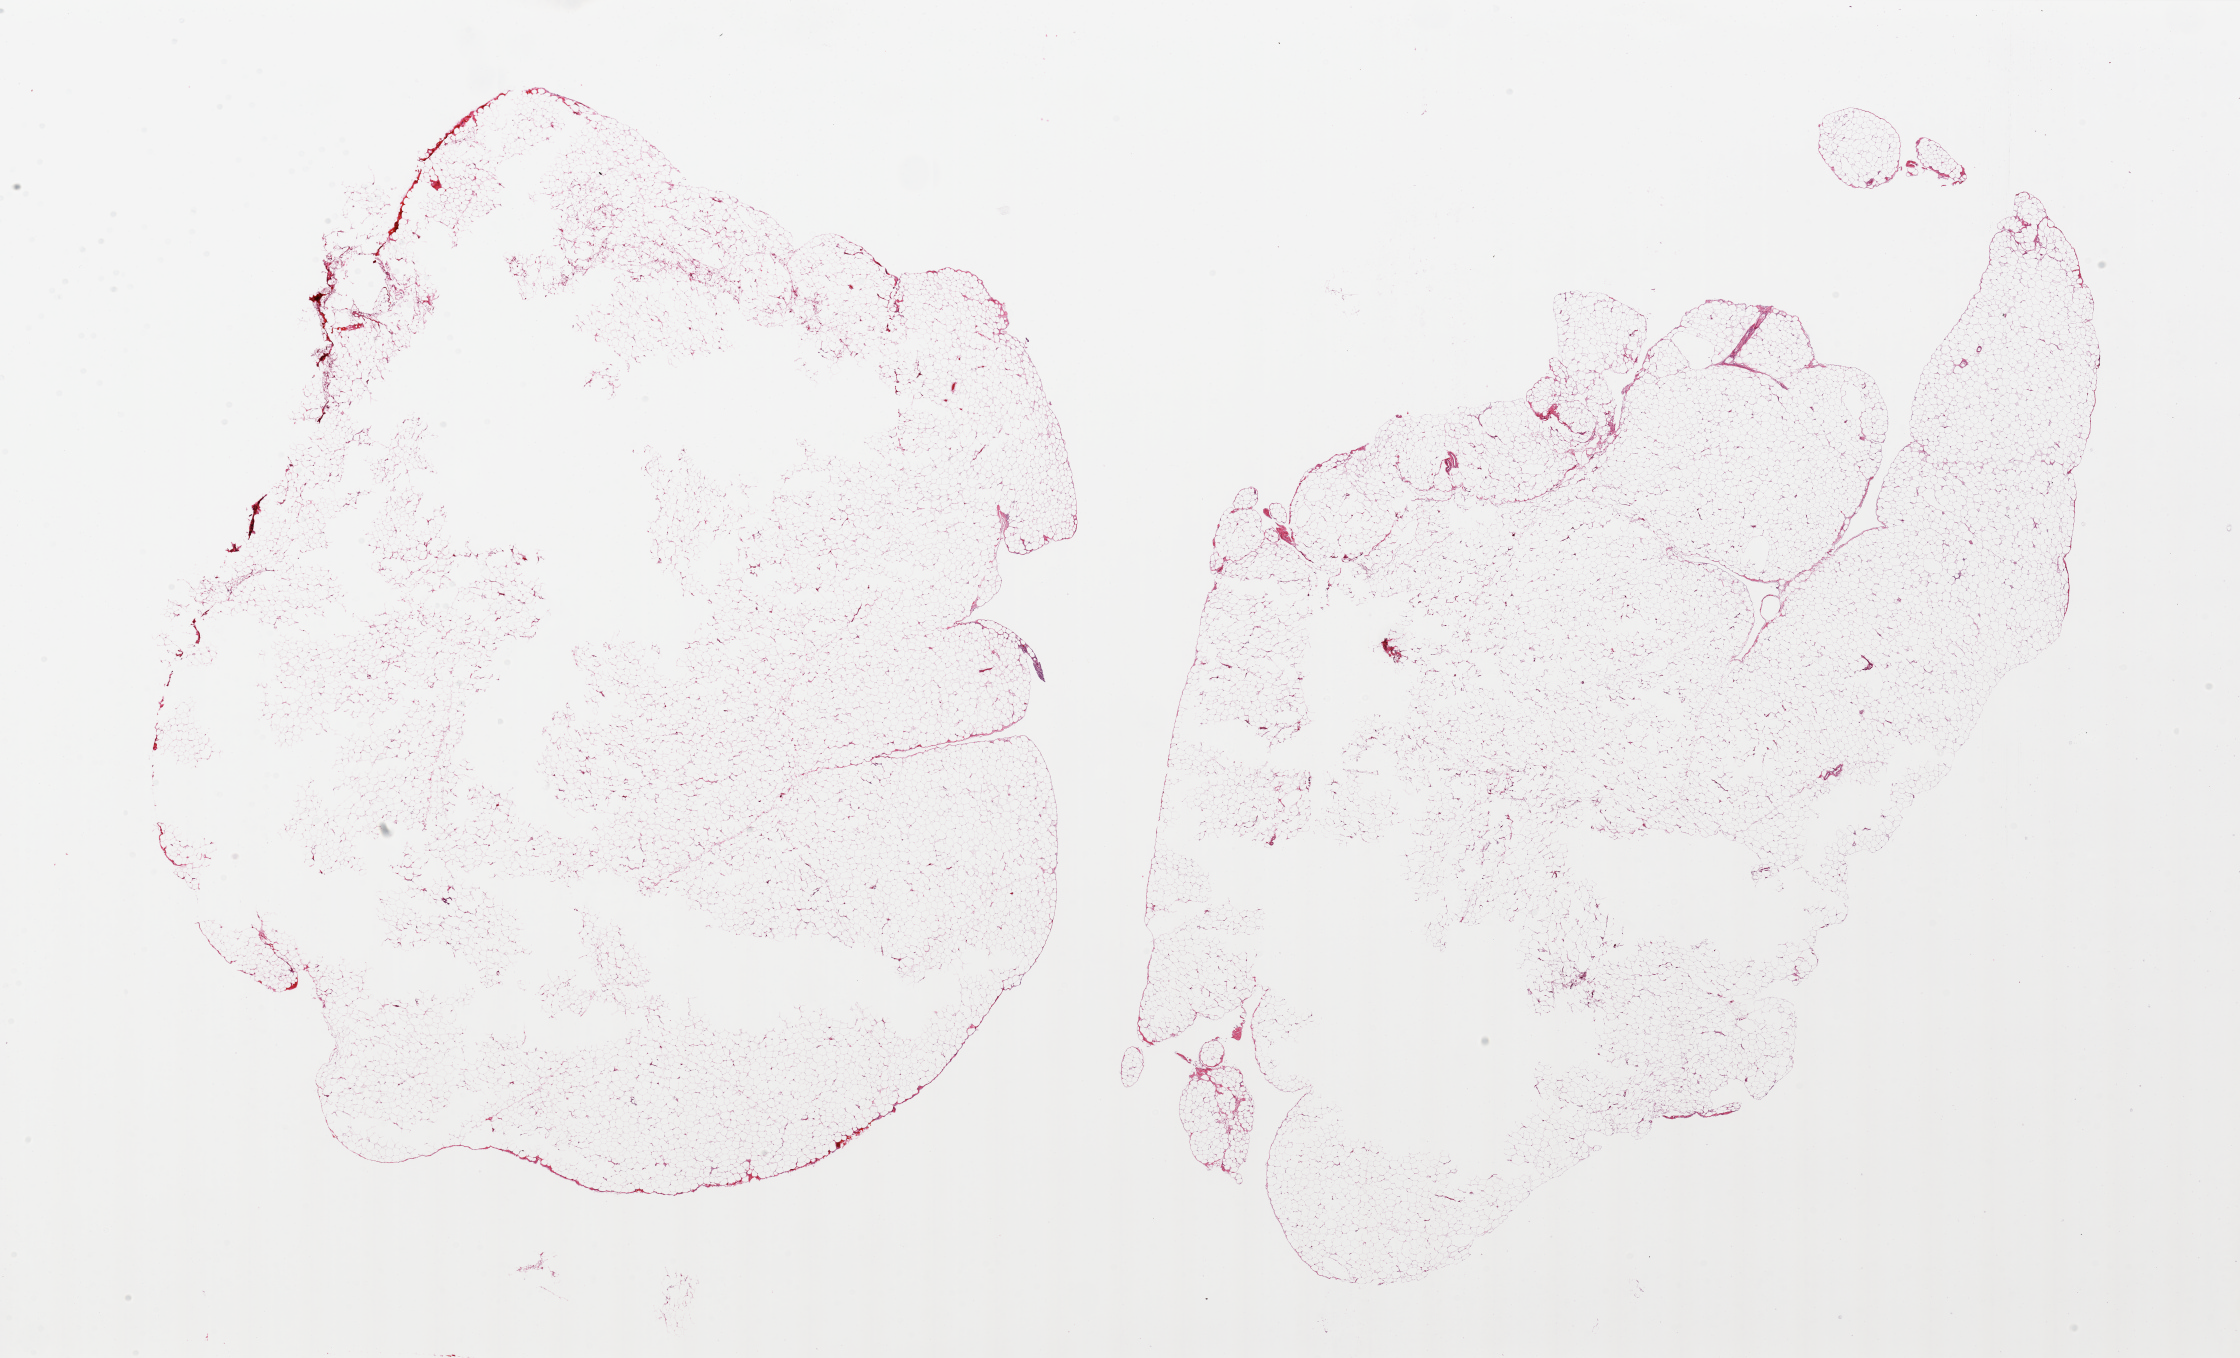
Whole-slide image, haematoxylin and eosin stain — shown as a low-resolution overview of the whole scanned area (about 35.4 x 21.5 mm). PAXgene-fixed, paraffin-embedded tissue. Section of omentum (target tissue). Donor tissue sample. Male donor.
Reviewer comment on this tissue sample: 2 pieces, central holes (? poor fixation), tissue is over-sized.